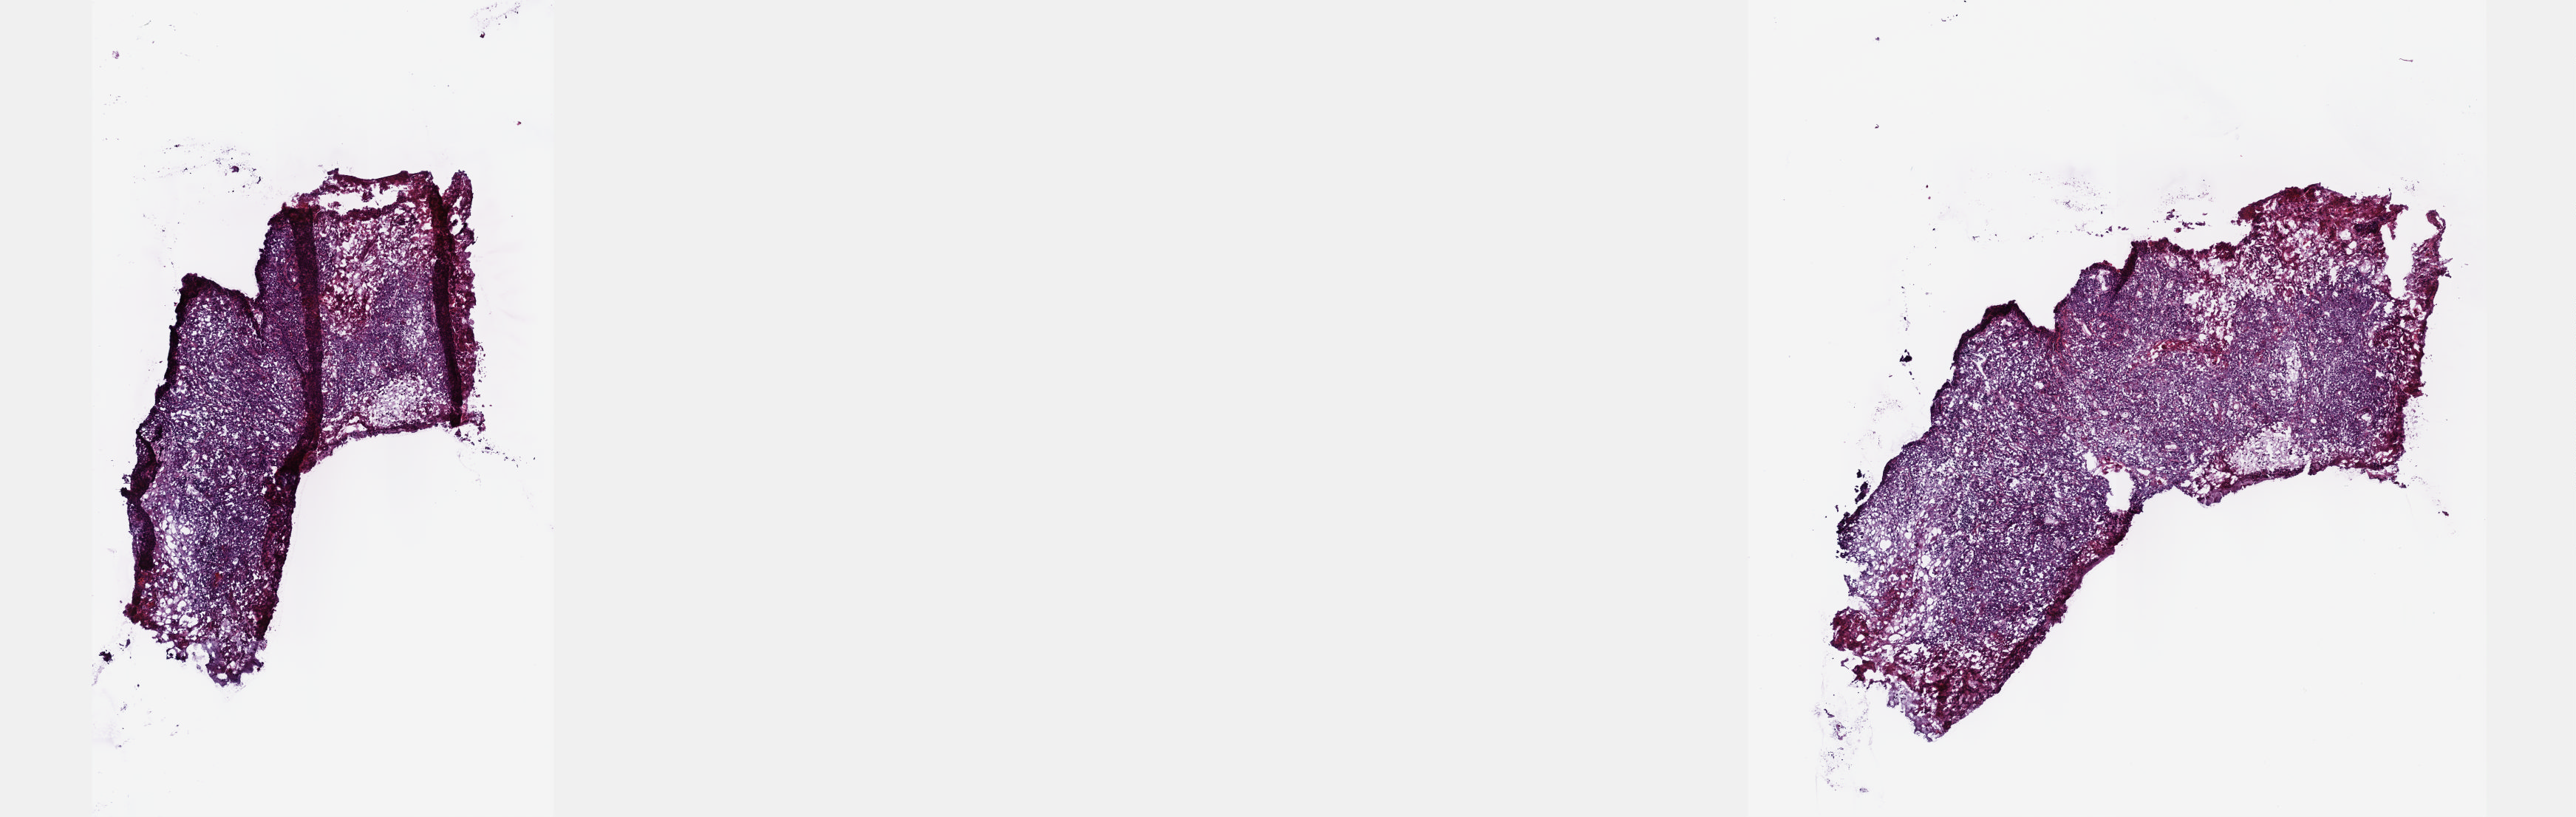
Digitized H&E-stained tissue section (whole slide), shown as a low-resolution overview of the whole scanned area (about 14.1 x 4.5 mm); frozen section from the top of the tissue portion; sample: primary tumour, cervix. Patient: female, age at initial diagnosis 48 years.
Diagnosis: Squamous cell carcinoma, keratinizing, NOS (cervix uteri).